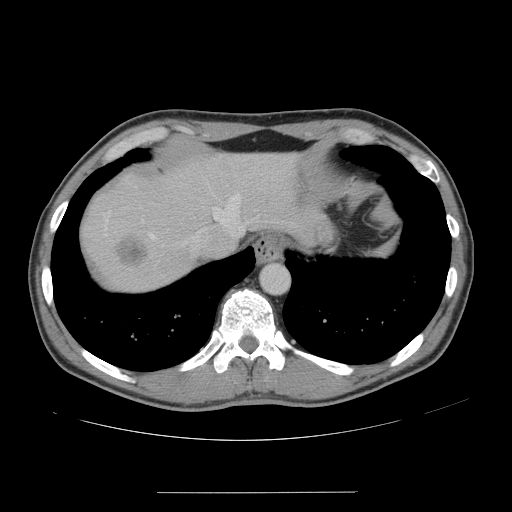
Contrast-enhanced abdominal CT, one axial slice; position 132 of 178 along the scan axis; 120 kVp; intravenous contrast given; soft-tissue window (W 400 / L 40 HU); 512 × 512 image matrix, field of view 401 × 401 mm. Male patient, age 53 years. Case-level facts recorded for this patient, not image findings: diagnosis: colorectal cancer liver metastases, imaged before liver resection; multiple liver metastases: yes; largest metastasis: 2.4 cm; disease in both lobes: no.
Annotated regions visible in this slice (outlined manually by an expert reader):
- hepatic veins: box from (x=105, y=193) to (x=250, y=247) px
- liver: (x=82, y=155)–(x=301, y=291)
- planned liver remnant (the part of the liver to remain after resection): (x=175, y=154)–(x=301, y=230)
- liver metastasis: (x=114, y=235)–(x=148, y=269)